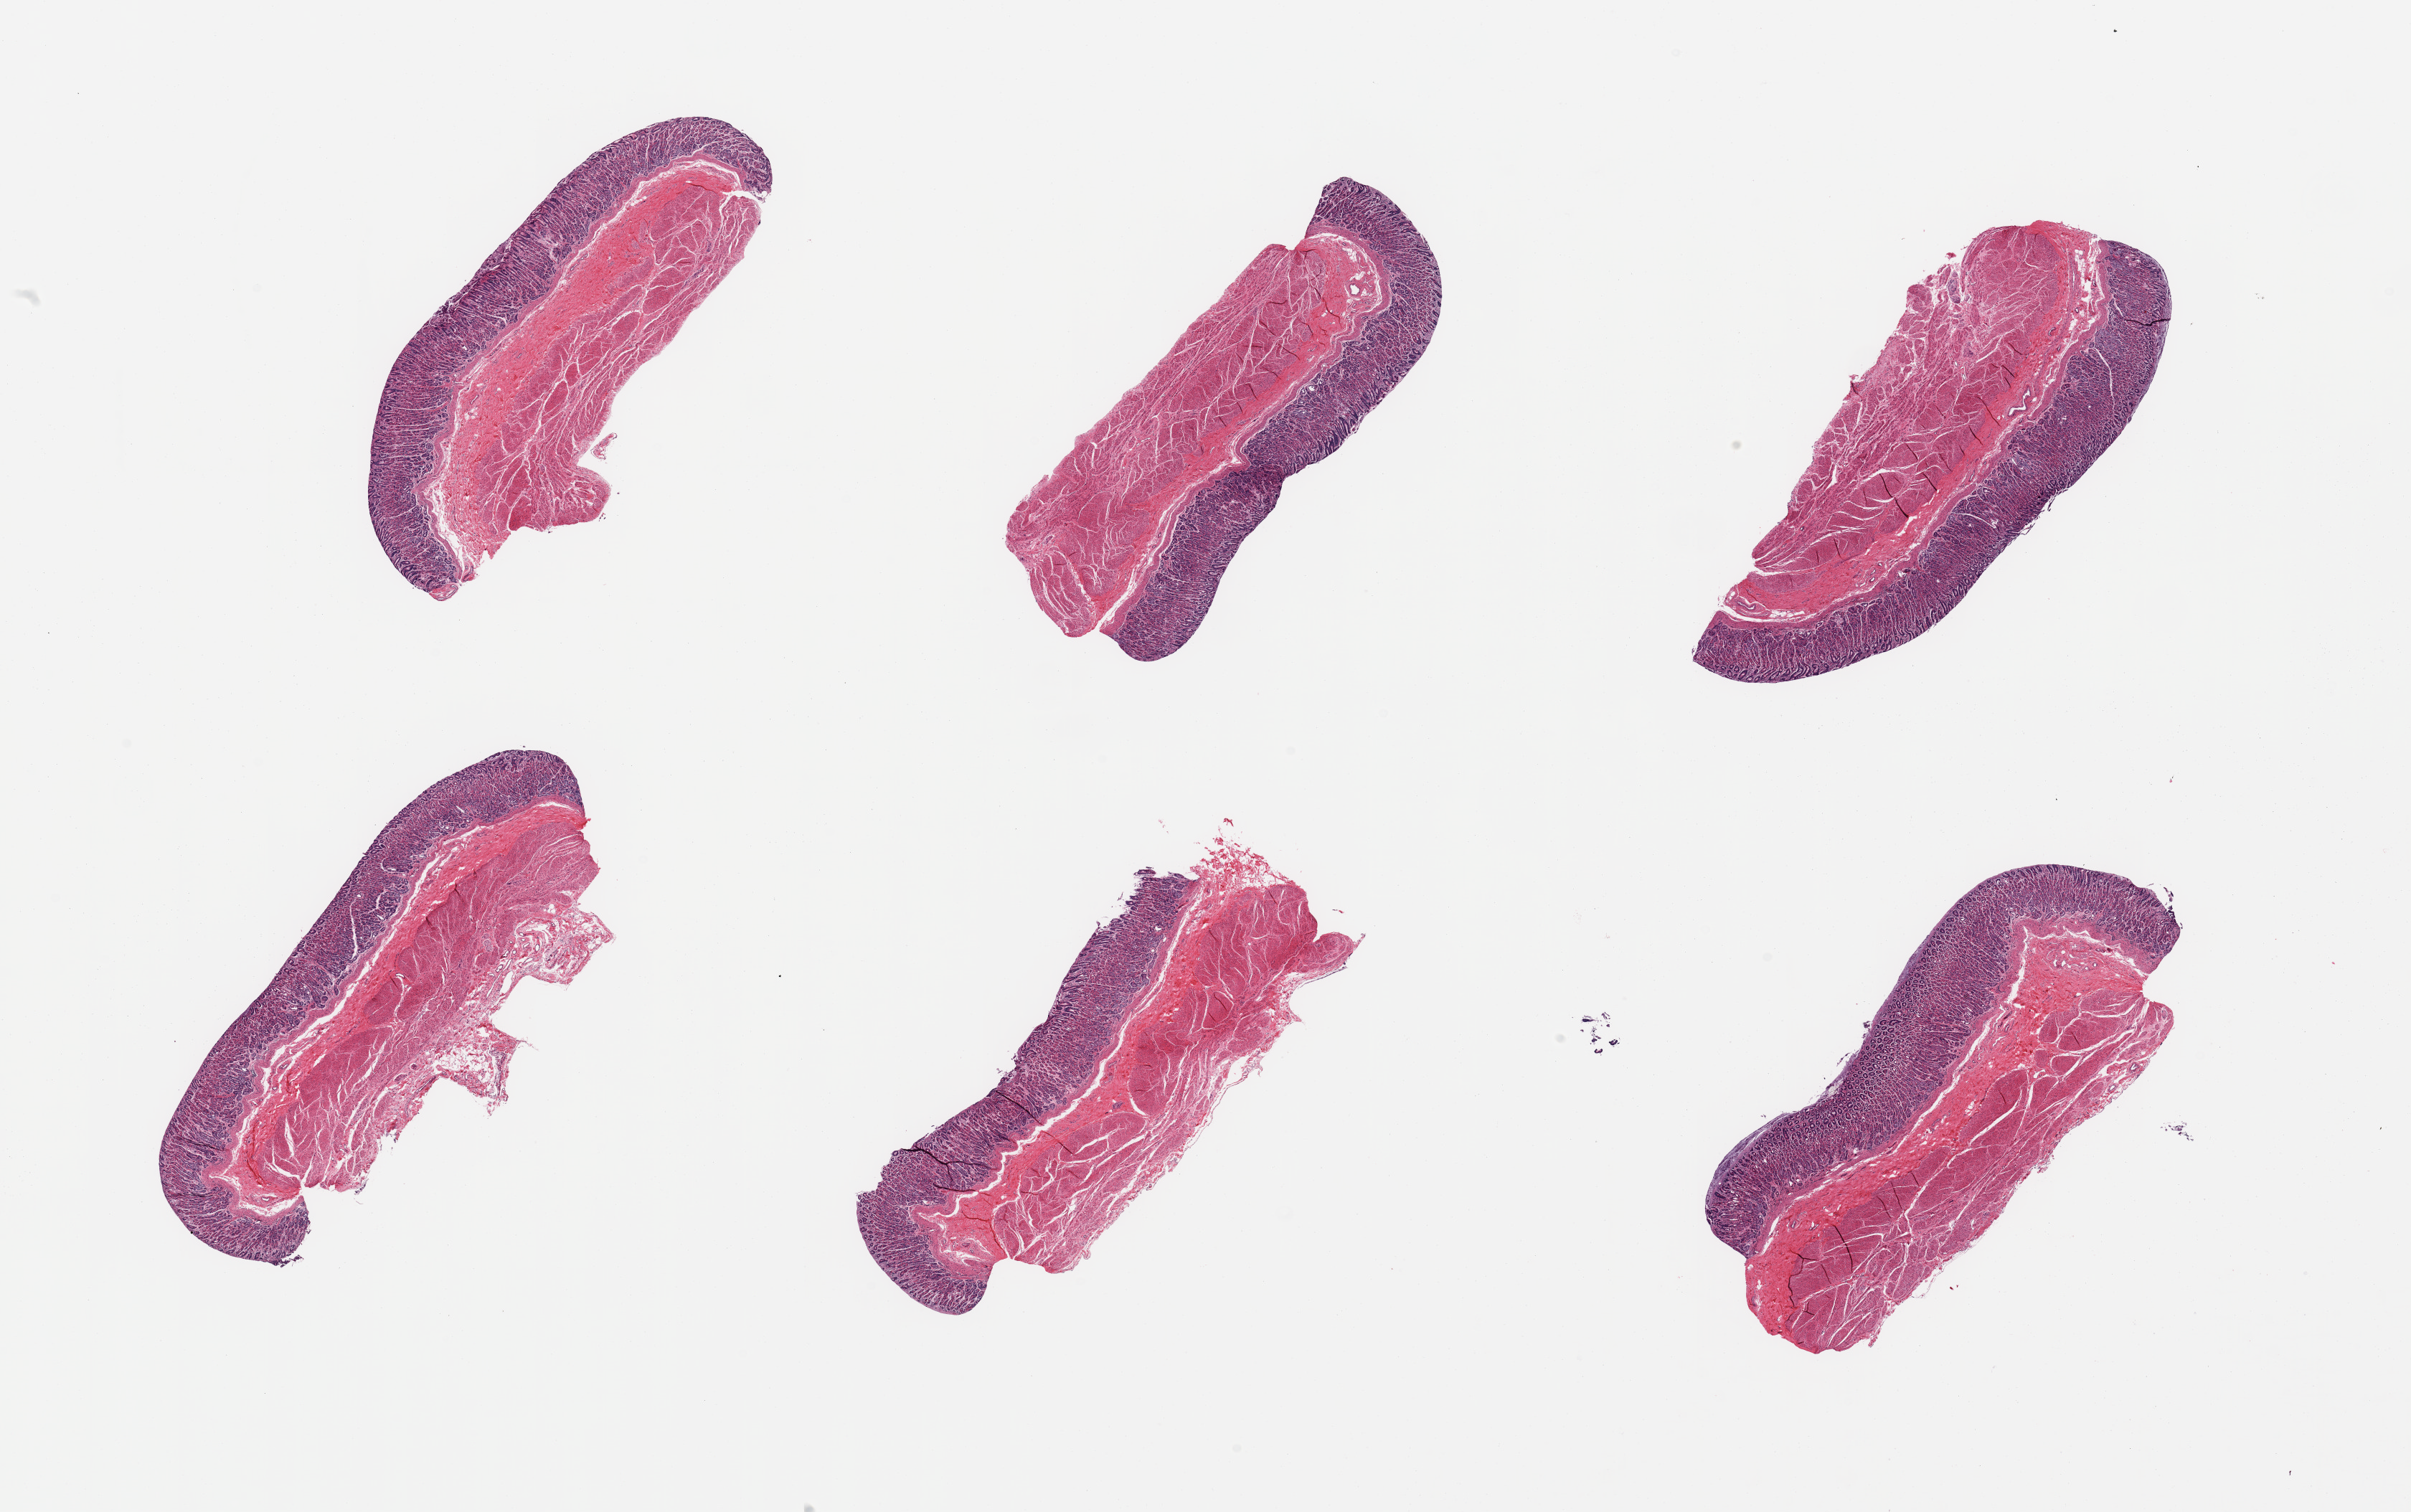
Whole-slide image, haematoxylin and eosin stain, brightfield — whole scanned area (about 26.6 x 16.7 mm, acquisition: 20x scan) shown as a low-resolution overview, PAXgene-fixed paraffin-embedded (PFPE) section, sampled site (target tissue): stomach, tissue donor sample.
• reviewer comment on this tissue sample: 6 pieces, mucosa well-preserved, up to ~1mm, ~30-40% thickness